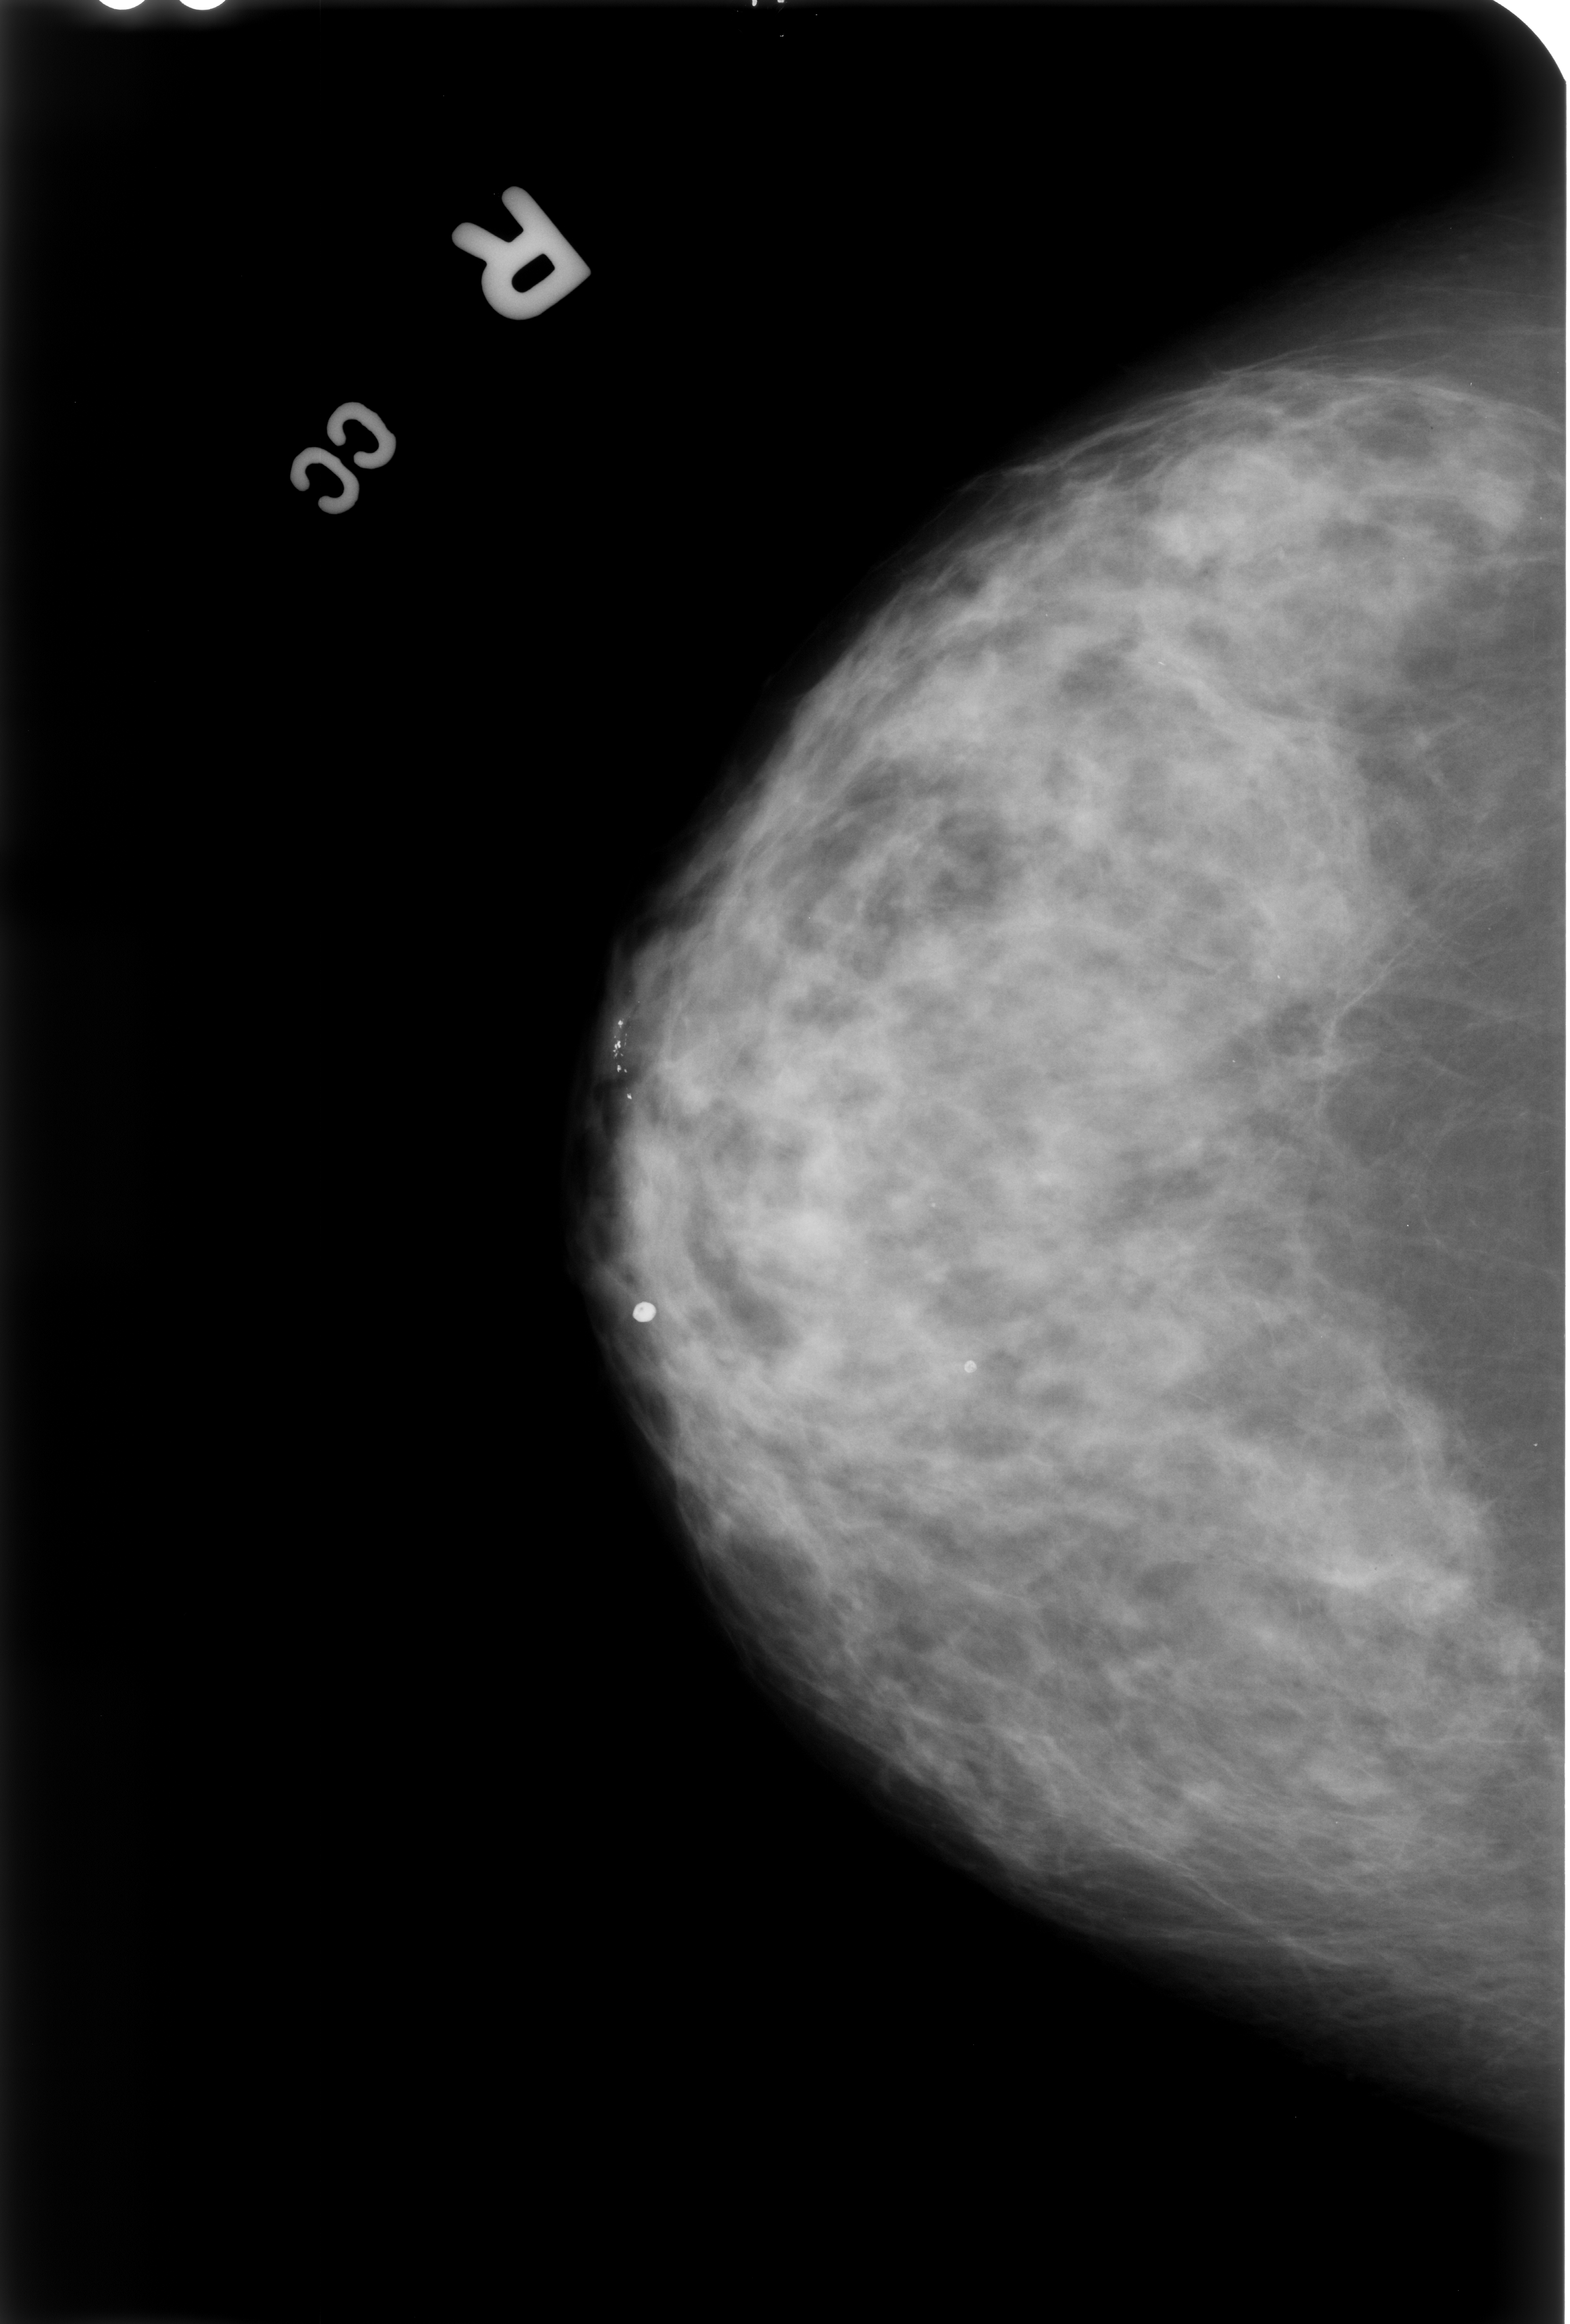
Scanned film-screen mammogram; right breast; craniocaudal (CC) view.
Radiologist-marked abnormalities on this image: Finding 1 of 2: calcifications, morphology lucent center; BI-RADS assessment category 2; subtlety rating 5 on a 1 (subtle) to 5 (obvious) scale; benign without callback (not worked up further). Finding 2 of 2: calcifications, morphology lucent center; BI-RADS assessment category 2; subtlety rating 5 on a 1 (subtle) to 5 (obvious) scale; benign without callback (not worked up further).